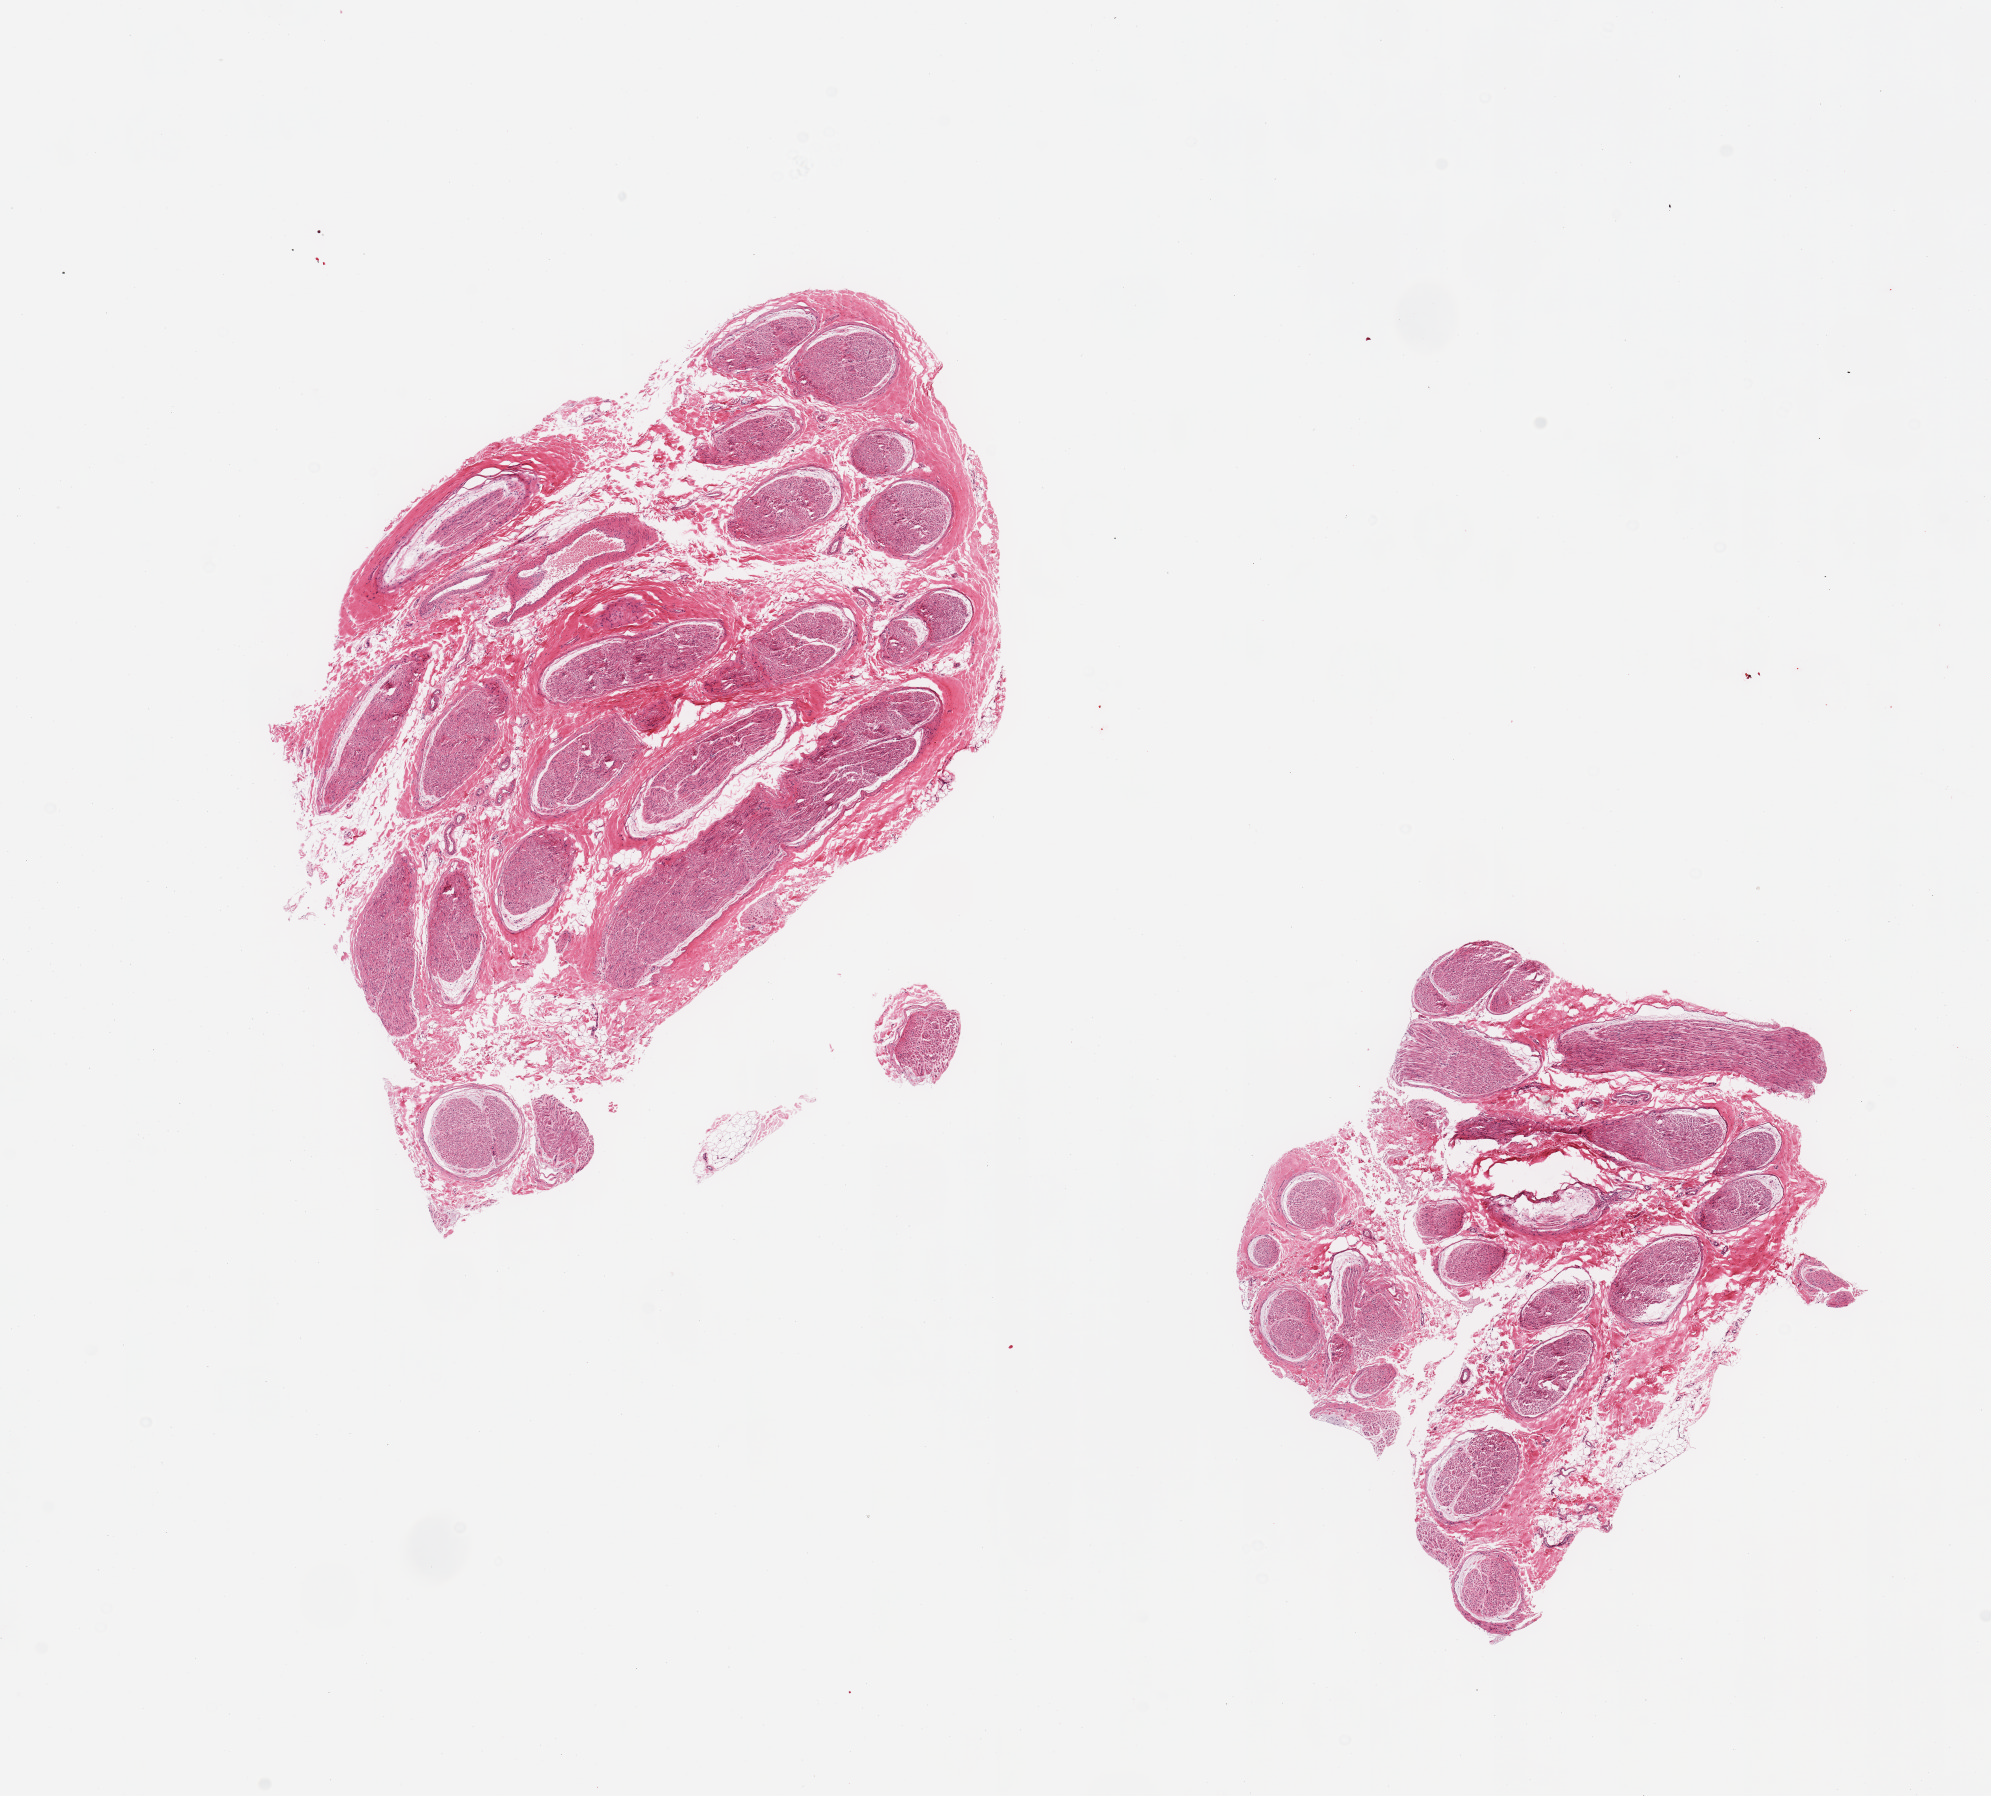
Whole-slide image, hematoxylin and eosin (H&E) stain — low-resolution overview of the scanned area, about 15.8 x 14.2 mm (acquisition: 20x scan); PAXgene-fixed paraffin-embedded (PFPE) section; sampled site (target tissue): tibial nerve; tissue donor sample. Male donor.
Pathologist's review note for this sample: 2 pieces.